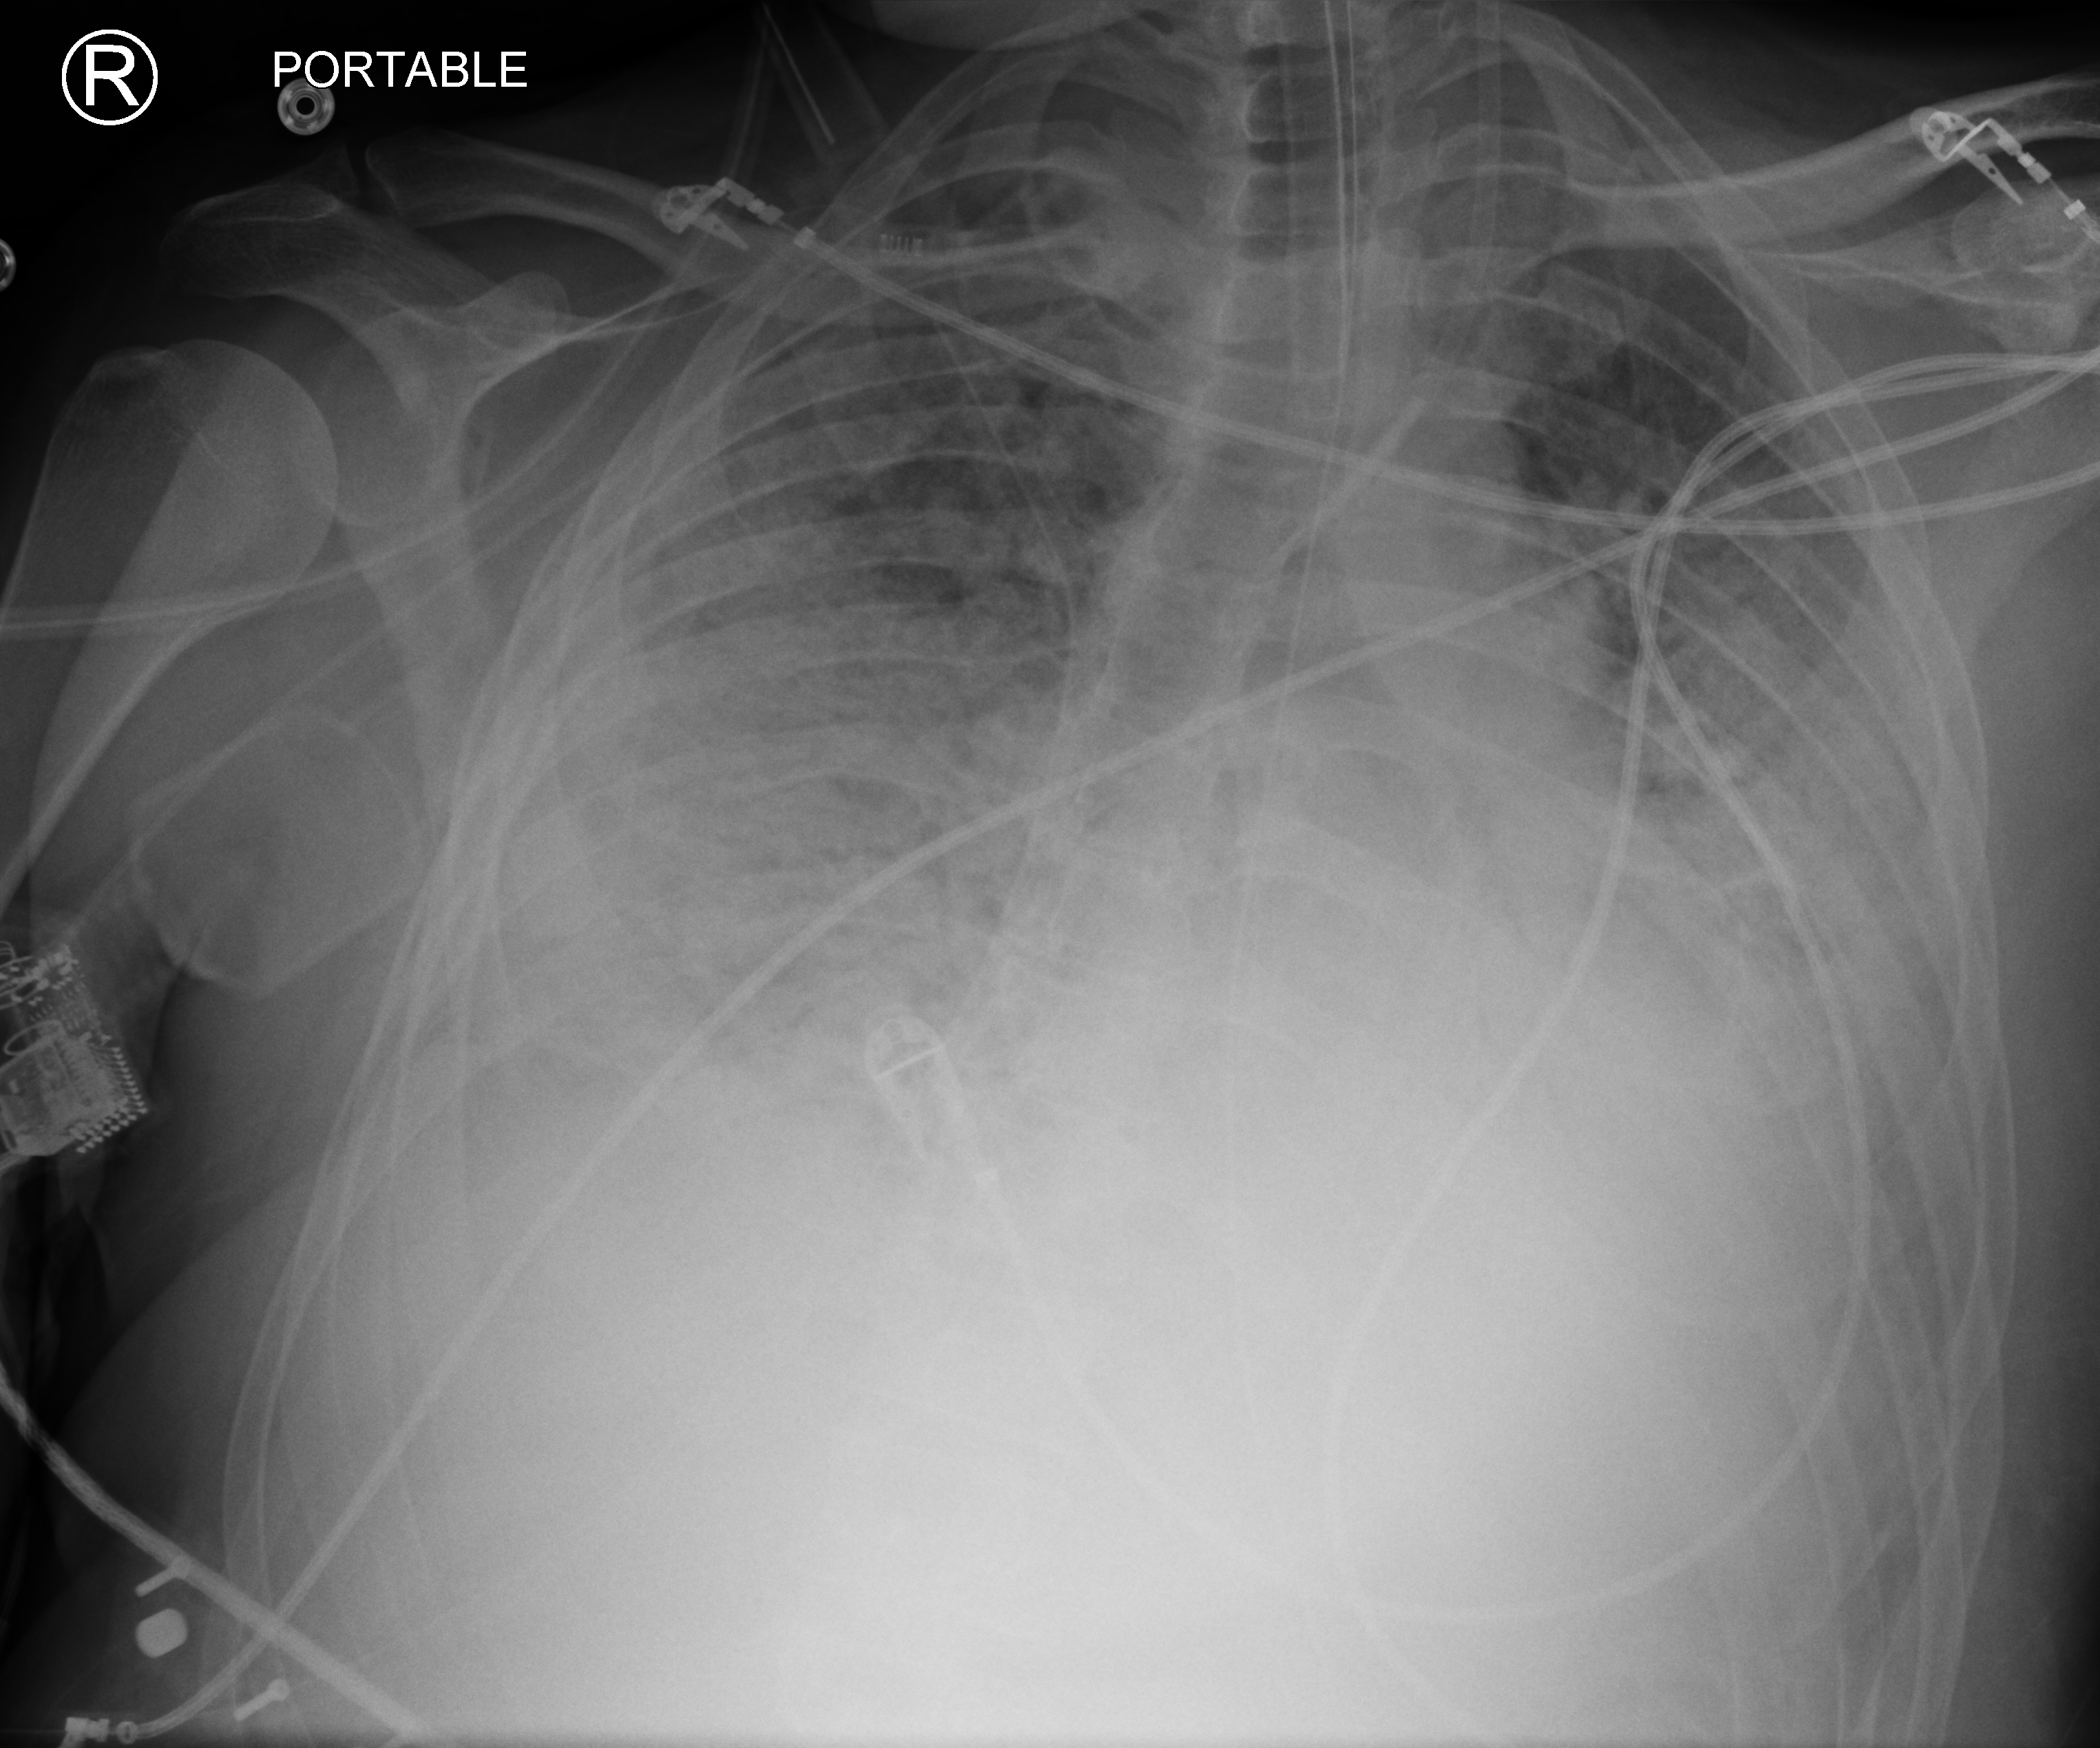
Bedside chest radiograph (computed radiography), anteroposterior (AP) projection. Male patient hospitalised with COVID-19, age 18–59 years.
From the hospital-stay record, not from the radiograph (when in the stay this image was taken is not recorded): mechanically ventilated during this hospital stay: yes; admitted to intensive care during this hospital stay: yes.